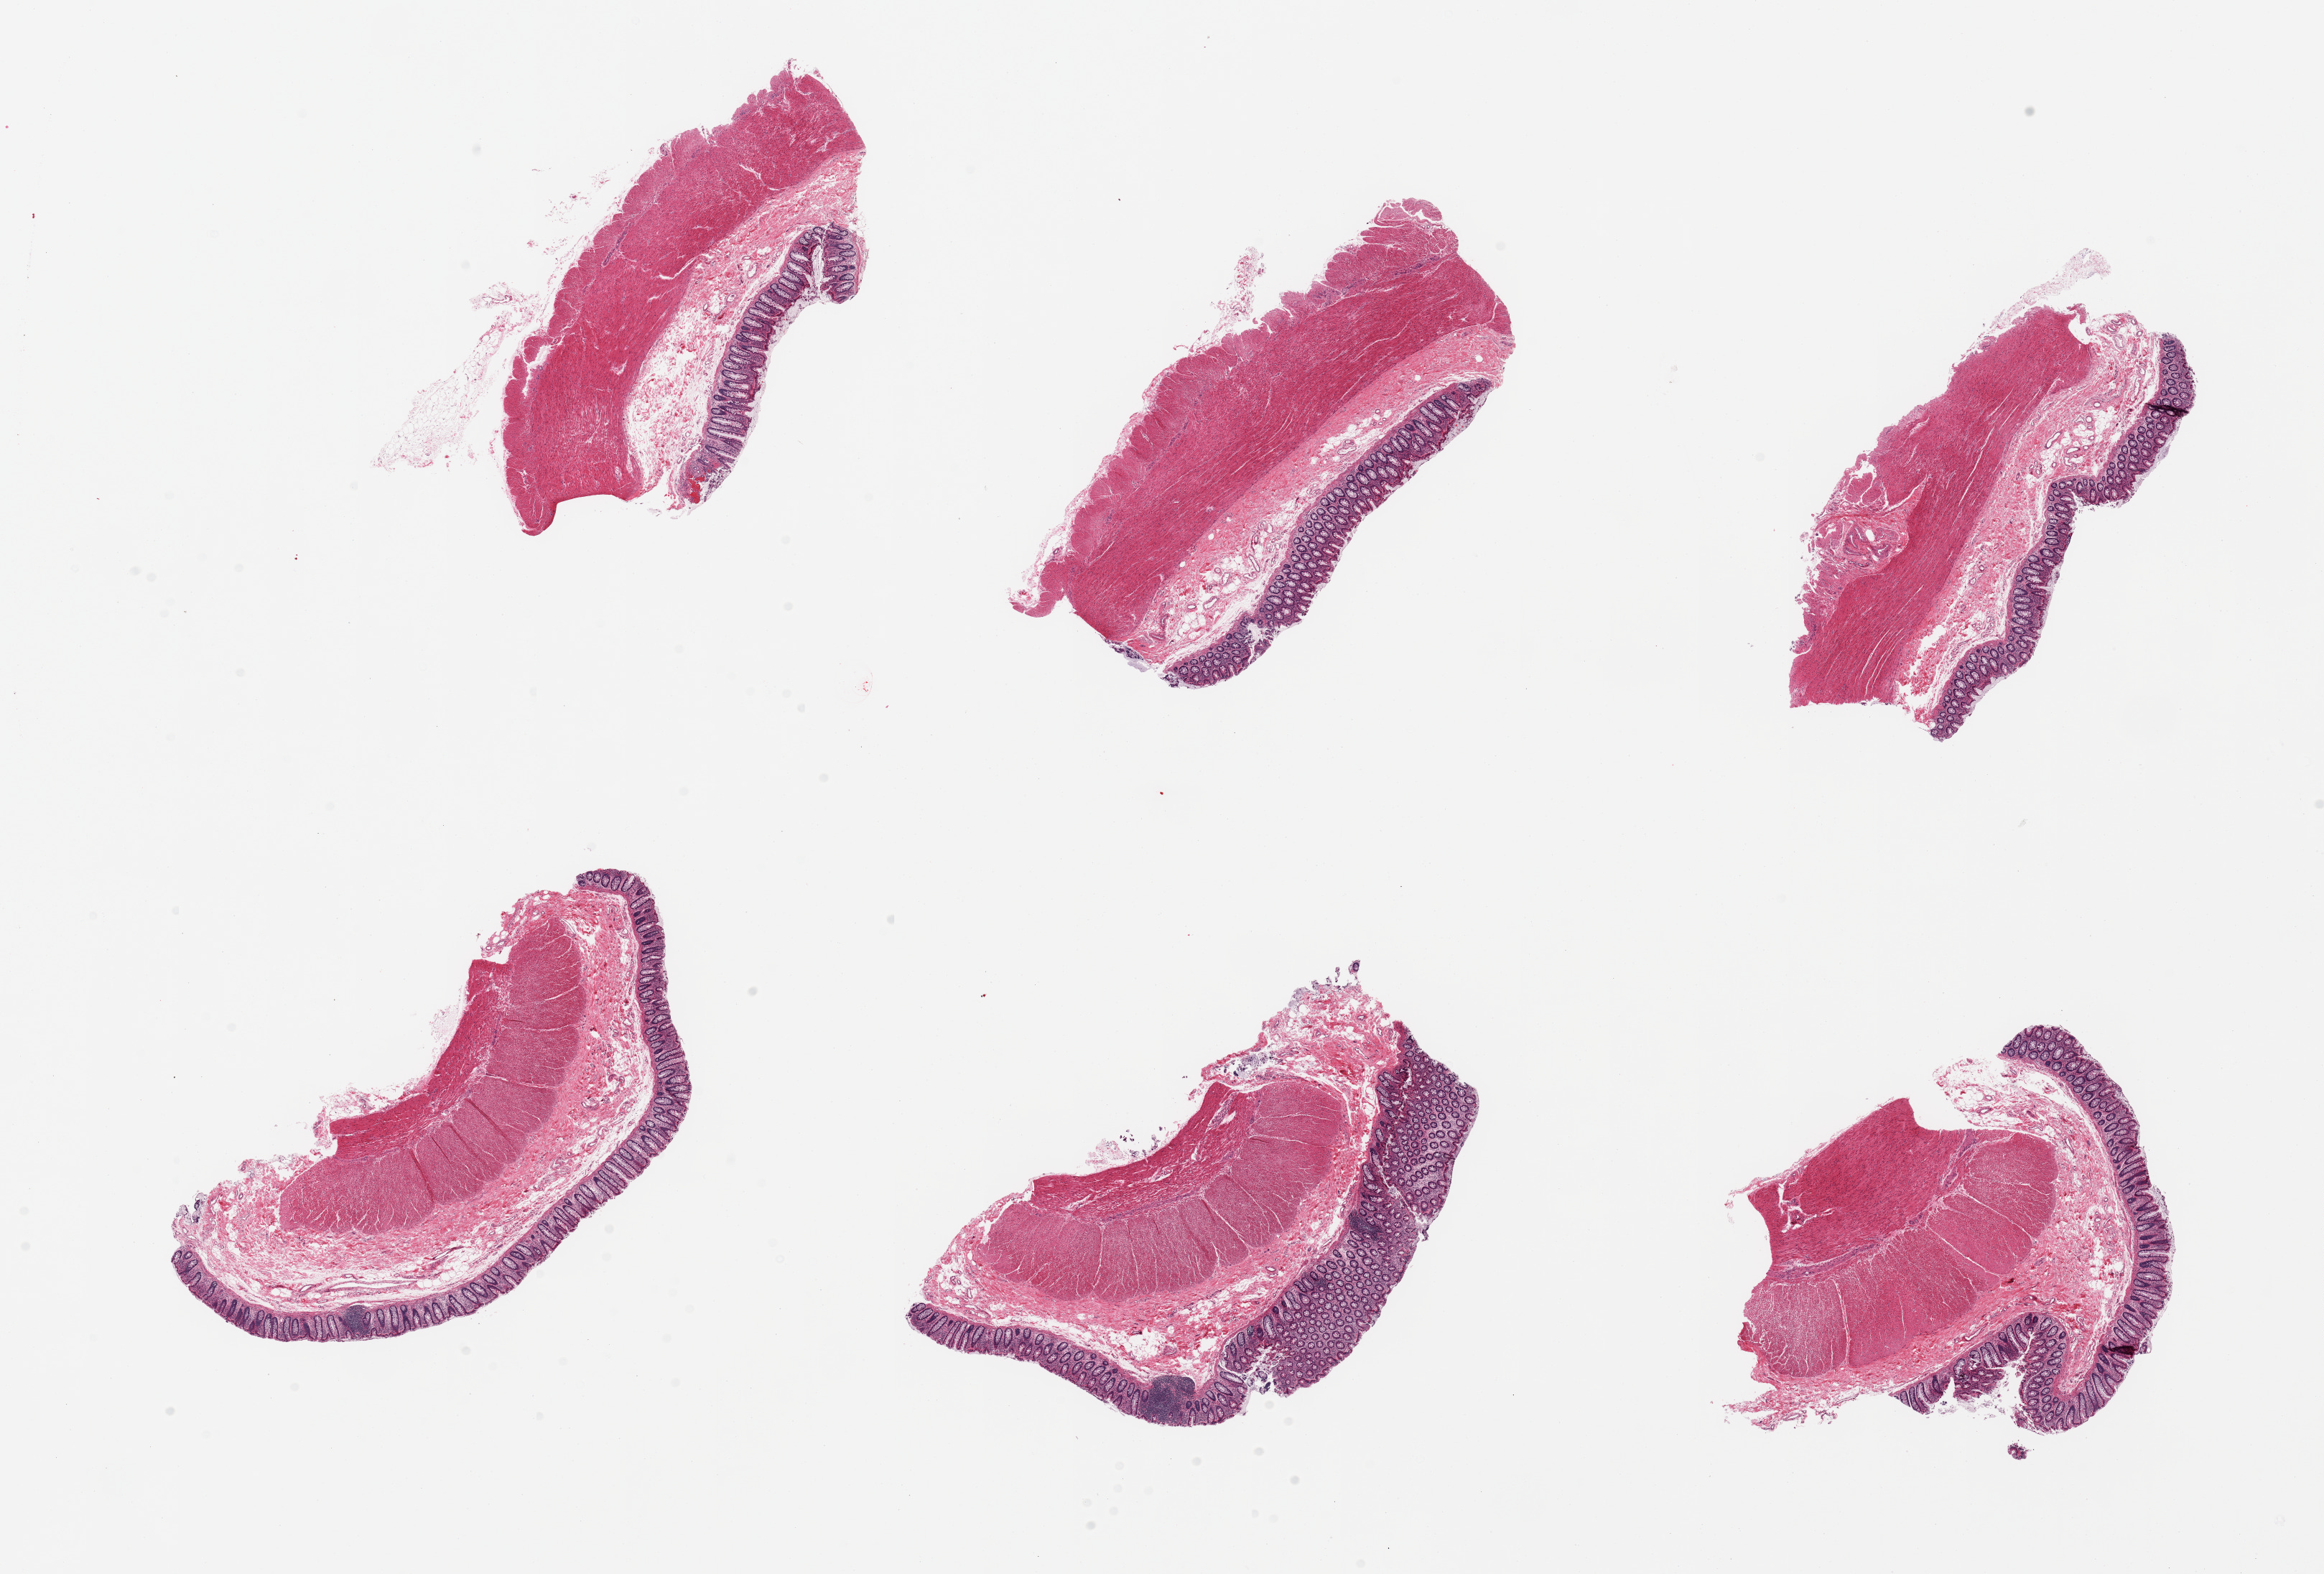
Haematoxylin and eosin whole-slide image — whole scanned area (about 25.6 x 17.3 mm, from a 20x scan) shown as a low-resolution overview. PAXgene-fixed, paraffin-embedded tissue. Target tissue: sigmoid colon. Tissue donor sample. Male donor.
Reviewer comment on this tissue sample: 6 pieces, extensive mucosa/ connective tissue; muscularis is <50%.